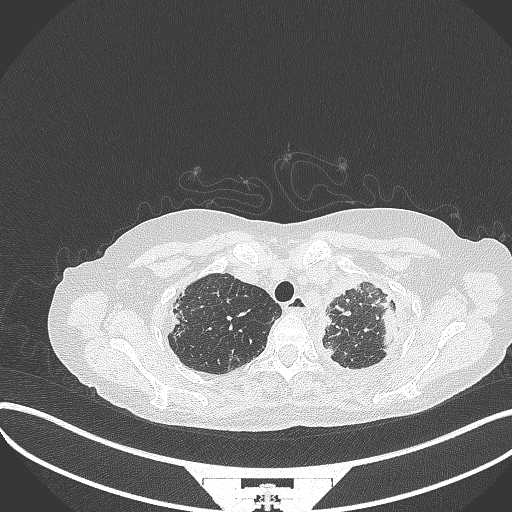
Chest CT, one axial slice. Slice 290 of 373 in the series (ordered by position). 120 kVp. Lung window (W 1500 / L -600 HU). 1 mm slice thickness. 512 × 512 image matrix, field of view 400 × 400 mm. Patient: female, 56 years. From the clinical record (not read from this slice): clinical TNM (as recorded): T1 N0 M0.
Annotated regions visible in this slice (bounding box drawn by a radiologist):
- lung tumour (recorded histology: adenocarcinoma): bounding box (x1, y1, x2, y2) in pixels: (372, 302, 405, 348)